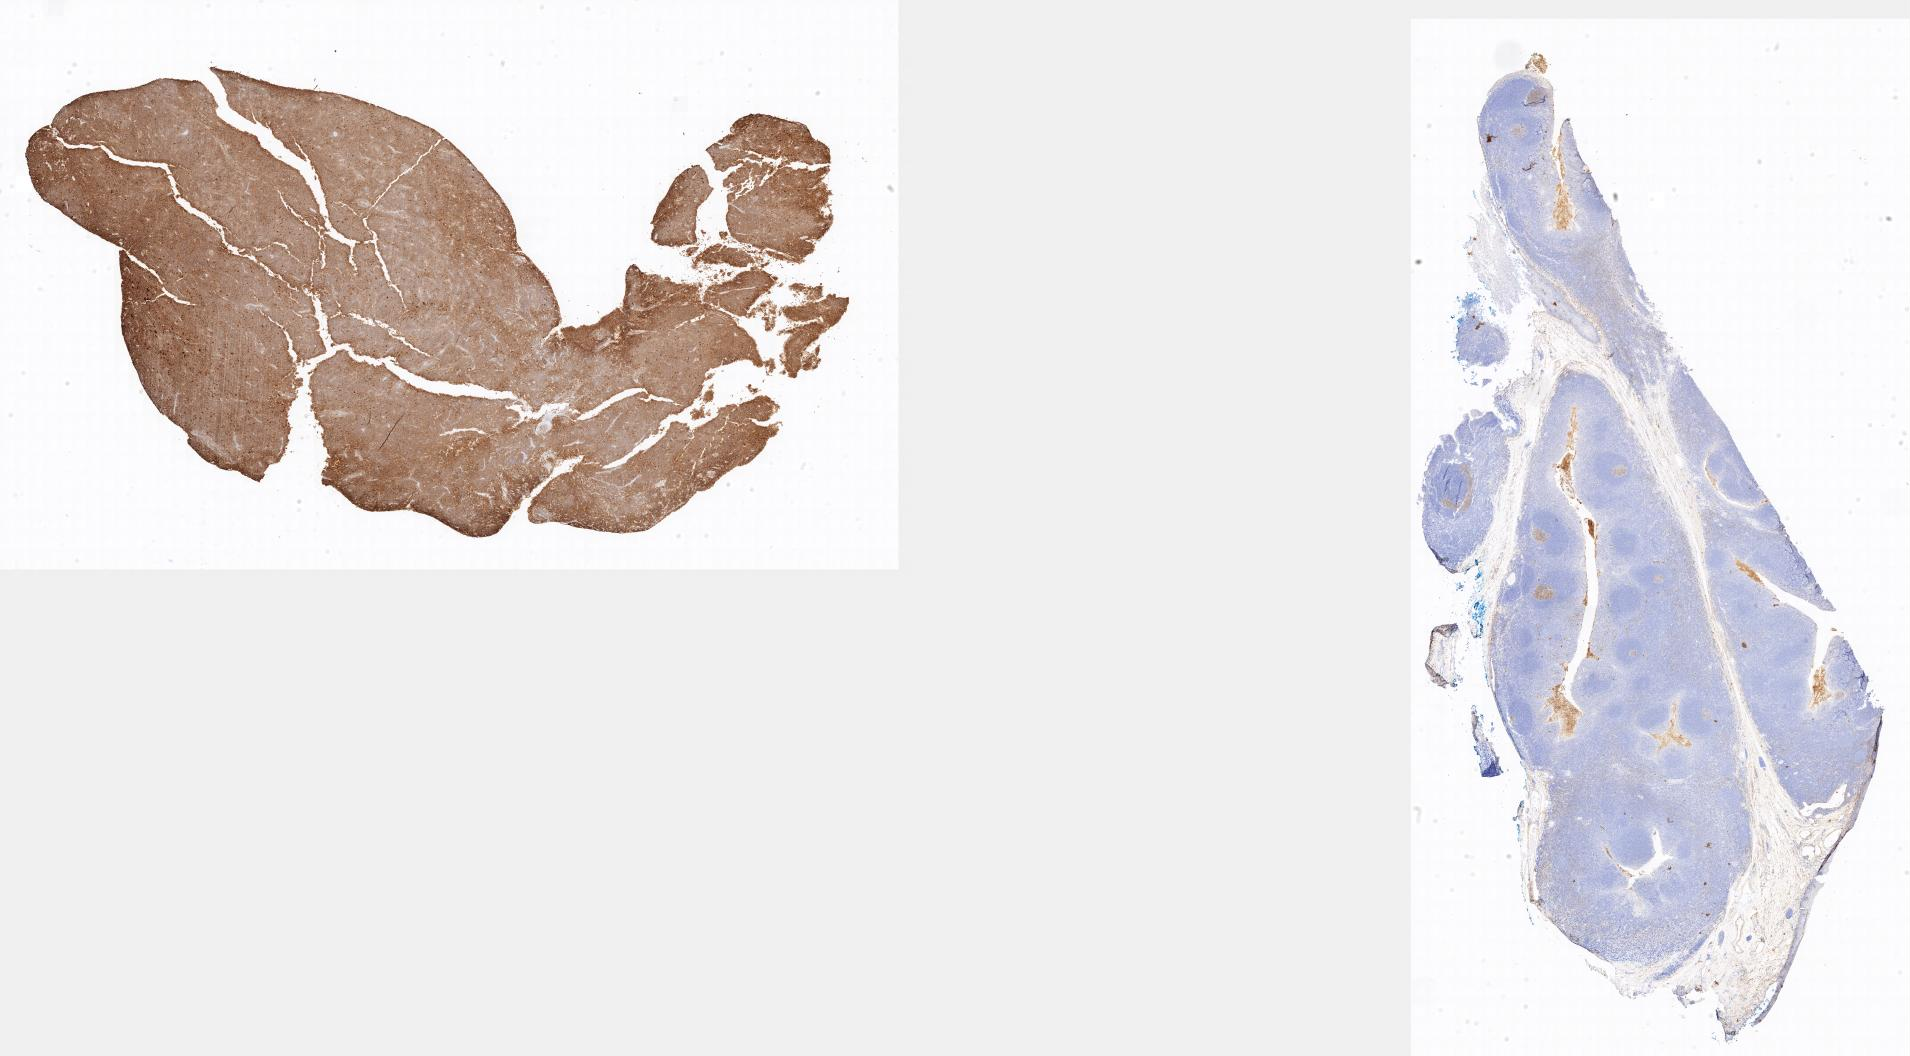
Immunohistochemistry (IHC) whole-slide image stained for CD10 — a low-resolution overview of the entire scanned area, specimen: tumor tissue, anatomic site: lymph node of head and neck. Male, age 5 years at initial diagnosis.
Diagnosis: Burkitt lymphoma, NOS.